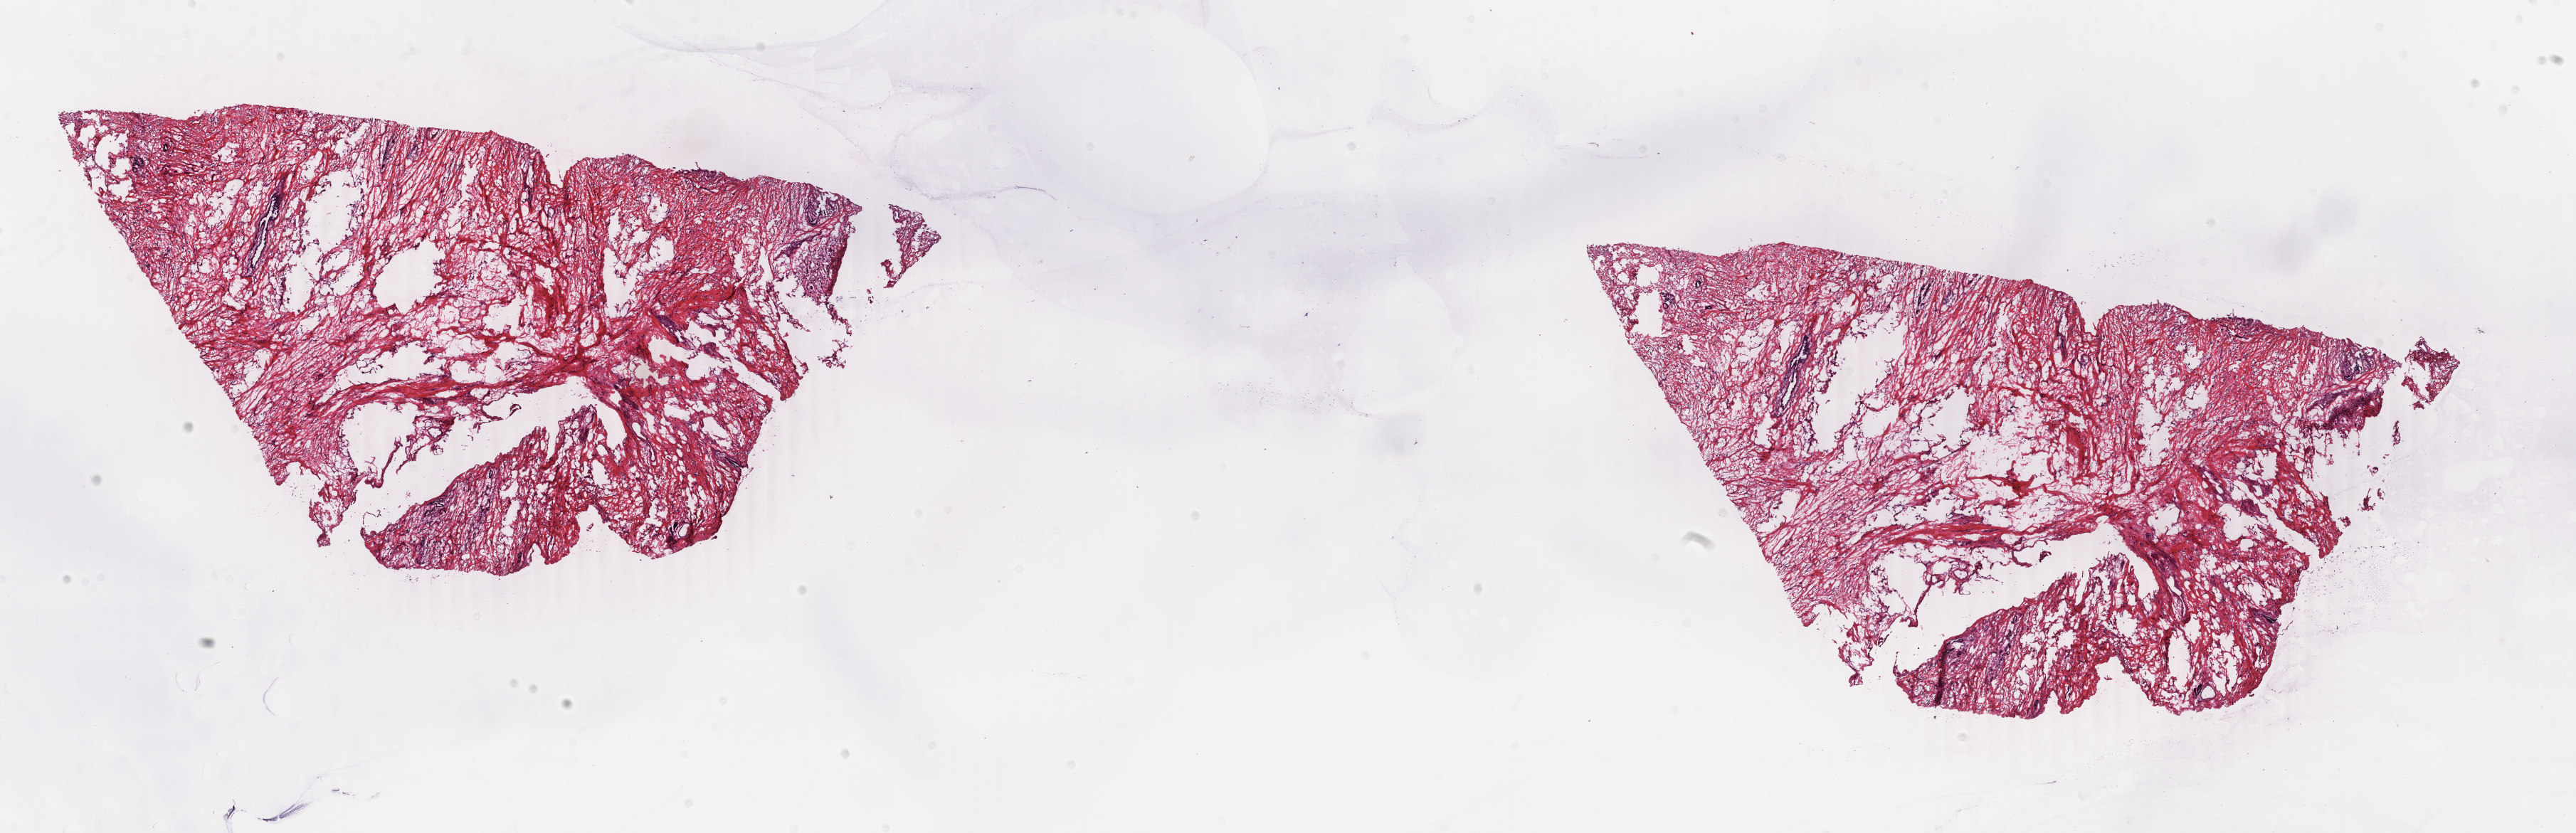
Digitized H&E-stained tissue section (whole slide) — shown as a low-resolution overview of the whole scanned area (about 28.8 x 9.3 mm). Frozen section. Primary tumour sample from the breast. Patient: female, age at initial diagnosis 68 years. Composition of this section per pathologist review: tumour cells 45%, tumour nuclei 60%, normal cells 10%, stromal cells 45%, necrosis 0%. Inflammatory infiltration, as recorded: lymphocyte infiltration 2%, monocyte infiltration 0%, neutrophil infiltration 0%.
- laterality: right
- AJCC pathologic stage: IIB (4th edition)
- TNM: T3 N0 (i-) M0
- pathologic diagnosis: Lobular carcinoma, NOS
- lymph nodes positive (case pathology): 0 of 14 examined